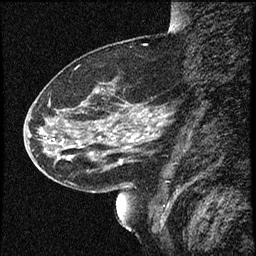
Breast MRI (dynamic contrast-enhanced), one sagittal slice. Position 24 of 60 along the scan axis. Dynamic contrast-enhanced study with each time point stored as its own series, time point 2 of 4 at this slice position (early post-contrast, ordered by acquisition time). 1.5 T. TE 4.2 ms, TR 16.7 ms. 256 × 256 image matrix, field of view 200 × 200 mm. Female patient, age 52 years. Case-level facts recorded for this patient, not image findings: setting: breast cancer imaged before/during neoadjuvant chemotherapy; receptor status: HER2-positive.
Annotated regions visible in this slice (semi-automatic segmentation, software-assisted and operator-edited):
- analysis volume of interest (the breast-tissue region the enhancement analysis was run in; not a lesion): bounding box (x1, y1, x2, y2) in pixels: (37, 79, 165, 181)
- tumour enhancement mask (voxels above the 100 % enhancement threshold inside the analysis volume of interest): (128, 134, 139, 139)